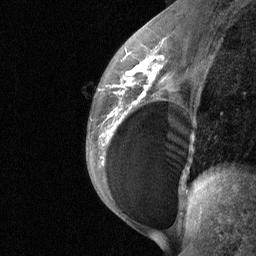
Breast MRI (dynamic contrast-enhanced), one sagittal slice; position 37 of 64 along the scan axis; dynamic contrast-enhanced study with each time point stored as its own series, time point 2 of 3 at this slice position (early post-contrast, ordered by acquisition time); 1.5 T; TE 4.8 ms, TR 27 ms; 2 mm slice thickness; 256 × 256 image matrix, field of view 200 × 200 mm. Patient: female, 34 years. From the clinical record (not read from this slice): setting: breast cancer imaged before/during neoadjuvant chemotherapy; receptor status: HR-positive, HER2-negative.
Structures marked on this image (semi-automatic segmentation, software-assisted and operator-edited):
- analysis volume of interest (the breast-tissue region the enhancement analysis was run in; not a lesion): bounding box (x1, y1, x2, y2) in pixels: (92, 50, 188, 185)
- tumour enhancement mask (voxels above the 90 % enhancement threshold inside the analysis volume of interest): (111, 55, 163, 116)